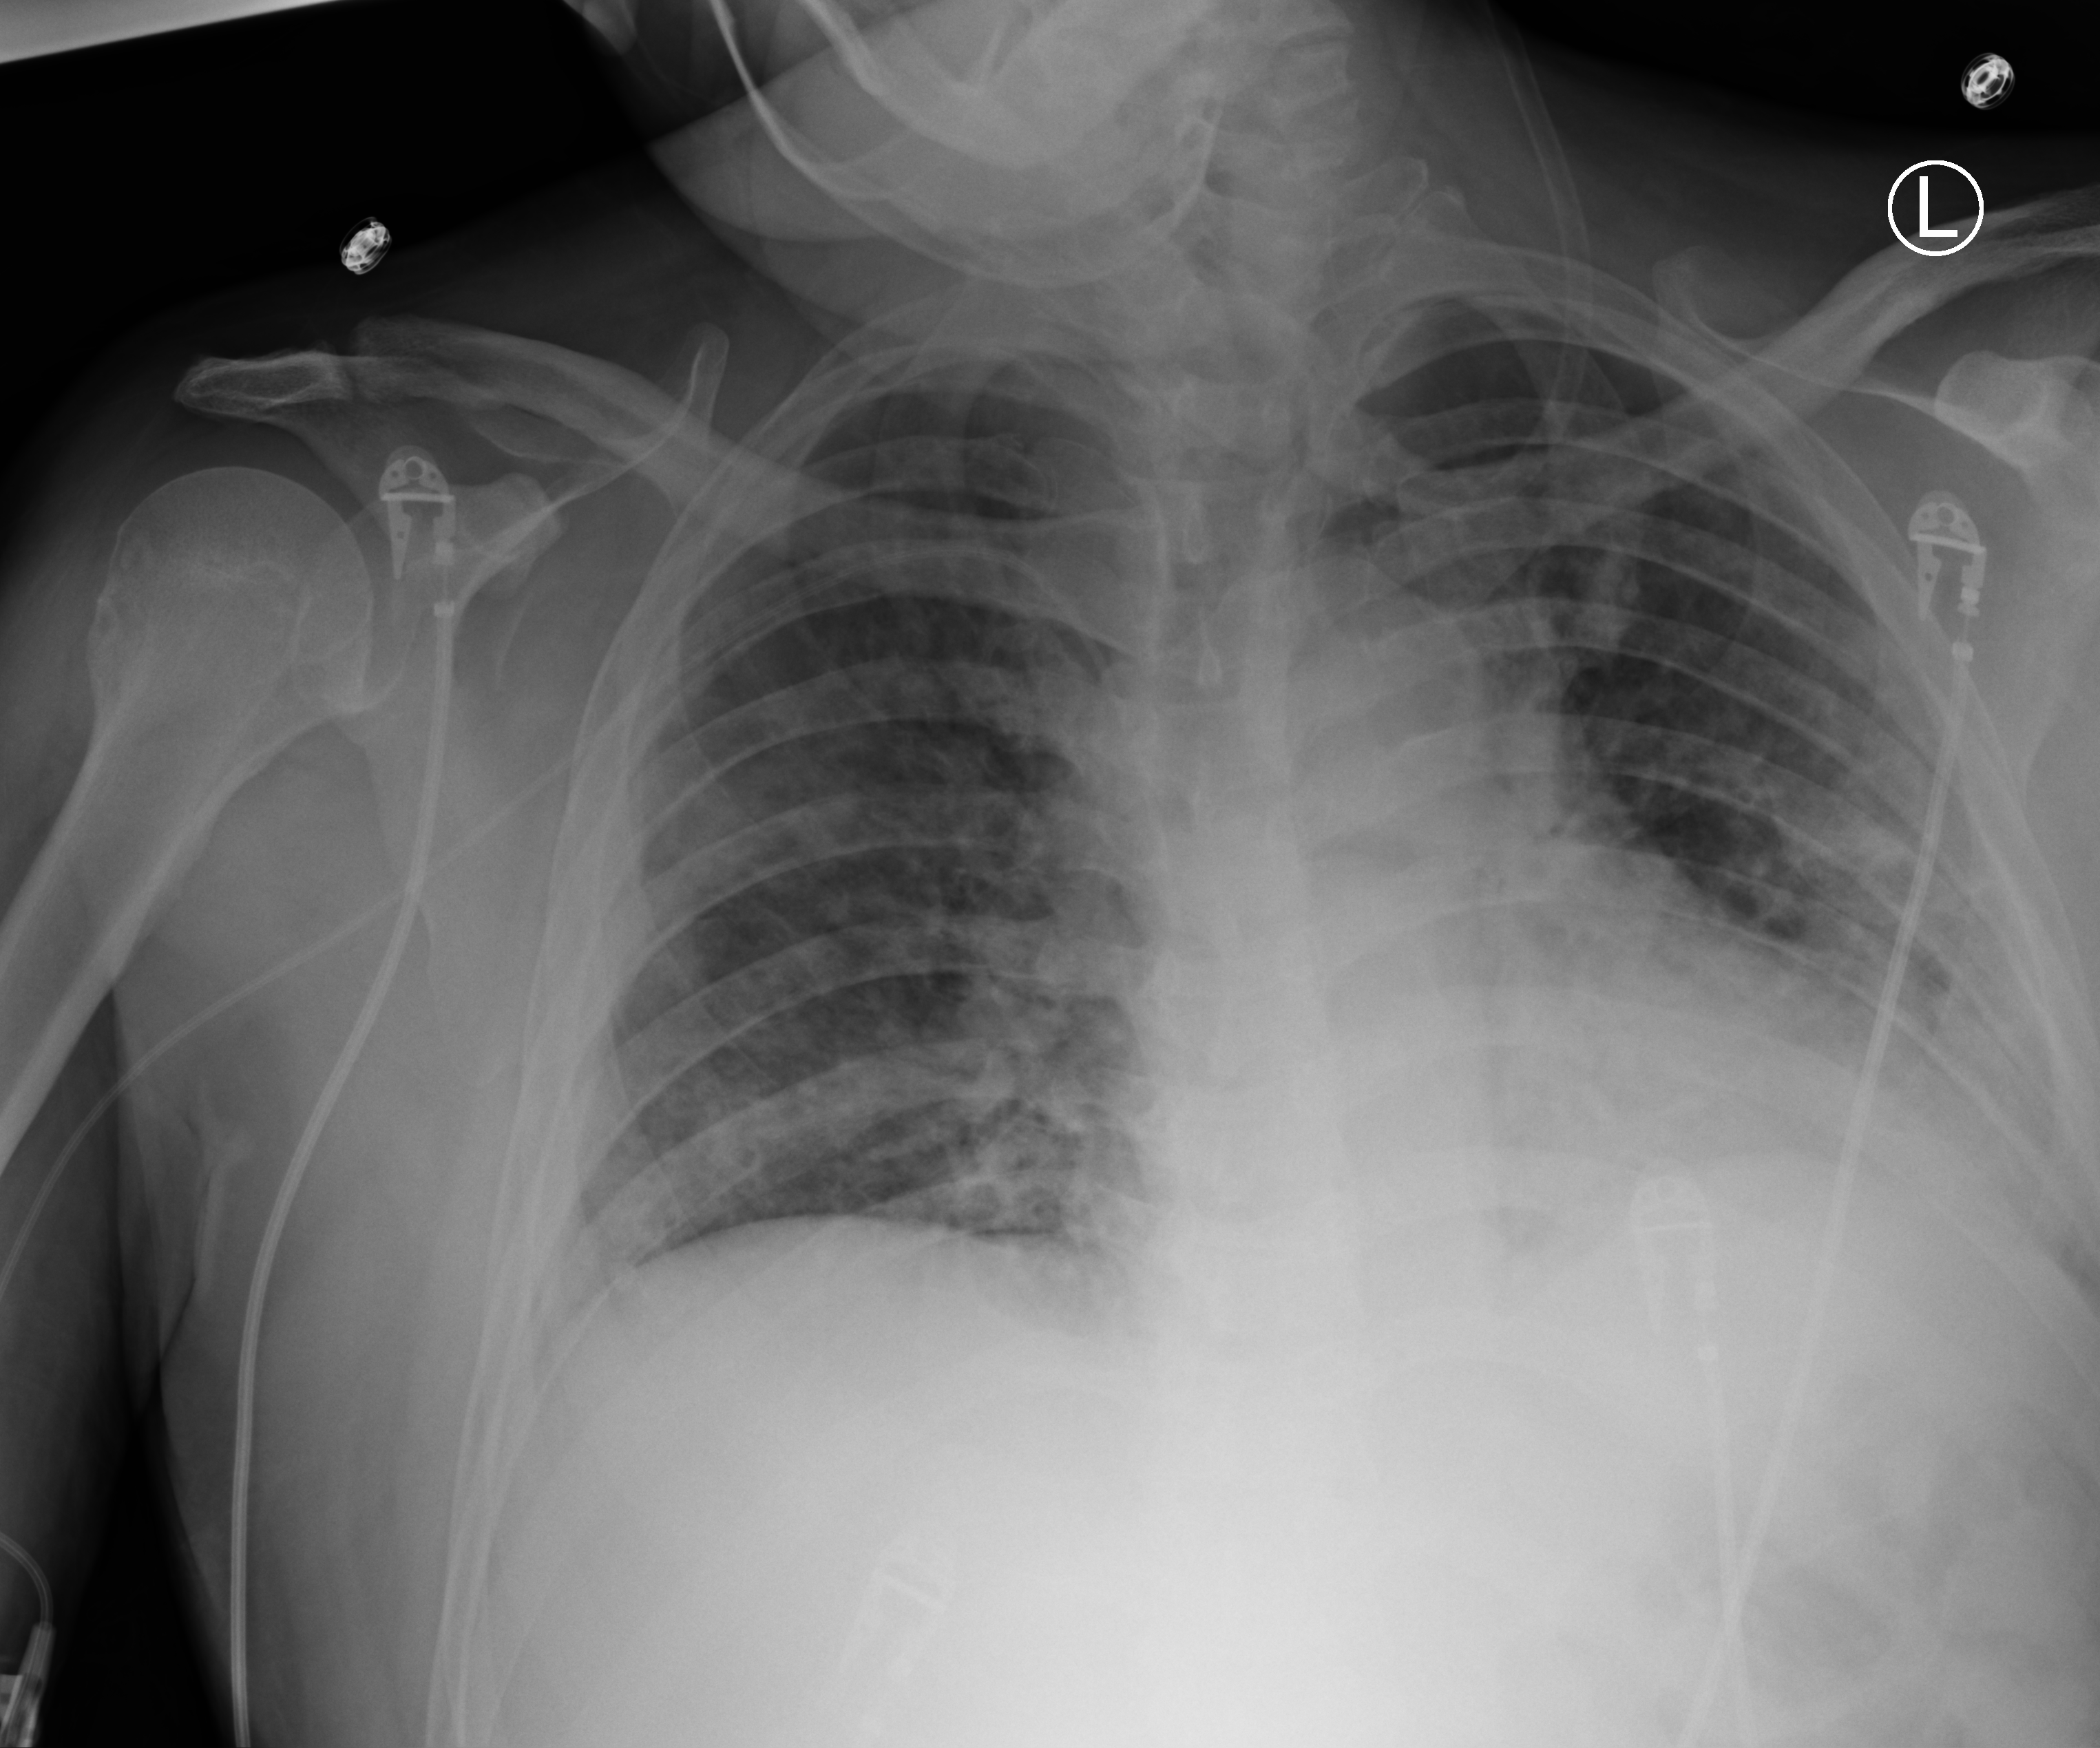
Chest X-ray (portable); anteroposterior (AP) projection. Patient hospitalised with COVID-19; male, aged 18–59 years.
Admission-level facts for this patient (not findings on this image; timing relative to this image not recorded):
- admitted to intensive care during this hospital stay: yes
- diabetes (admission record): yes